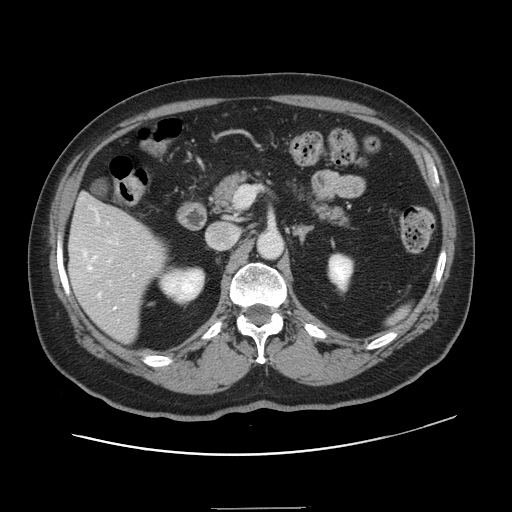
Contrast-enhanced abdominal CT, one axial slice; 120 kVp; intravenous contrast given; soft-tissue window (W 400 / L 40 HU); 2.5 mm slice thickness; 512 × 512 image matrix. Male patient, age 62 years. From the clinical record (not read from this slice): diagnosis: colorectal cancer liver metastases, imaged before liver resection; multiple liver metastases: yes; largest metastasis: 2.7 cm.
Annotated regions visible in this slice (outlined manually by an expert reader):
- hepatic veins: bounding box [x1, y1, x2, y2] px = [83, 207, 134, 297]
- liver: [70, 195, 166, 341]
- planned liver remnant (the part of the liver to remain after resection): [75, 195, 123, 222]
- portal vein (with intrahepatic branches): [108, 240, 118, 263]